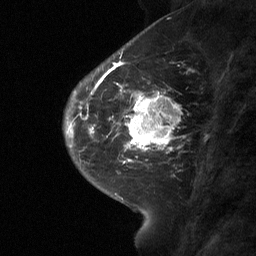
Breast MRI (dynamic contrast-enhanced), one sagittal slice; position 22 of 64 along the scan axis; dynamic contrast-enhanced study with each time point stored as its own series, time point 2 of 3 at this slice position (early post-contrast, ordered by acquisition time); 1.5 T; TE 4.8 ms, TR 27 ms; 256 × 256 image matrix, field of view 180 × 180 mm. Female patient, age 42 years. Case-level facts recorded for this patient, not image findings: setting: breast cancer imaged before/during neoadjuvant chemotherapy; receptor status: triple-negative.
Annotated regions visible in this slice (semi-automatic segmentation, software-assisted and operator-edited):
- analysis volume of interest (the breast-tissue region the enhancement analysis was run in; not a lesion): bounding box <115,85,181,160> (left, top, right, bottom; pixels)
- tumour enhancement mask (voxels above the 90 % enhancement threshold inside the analysis volume of interest): <116,85,174,160>